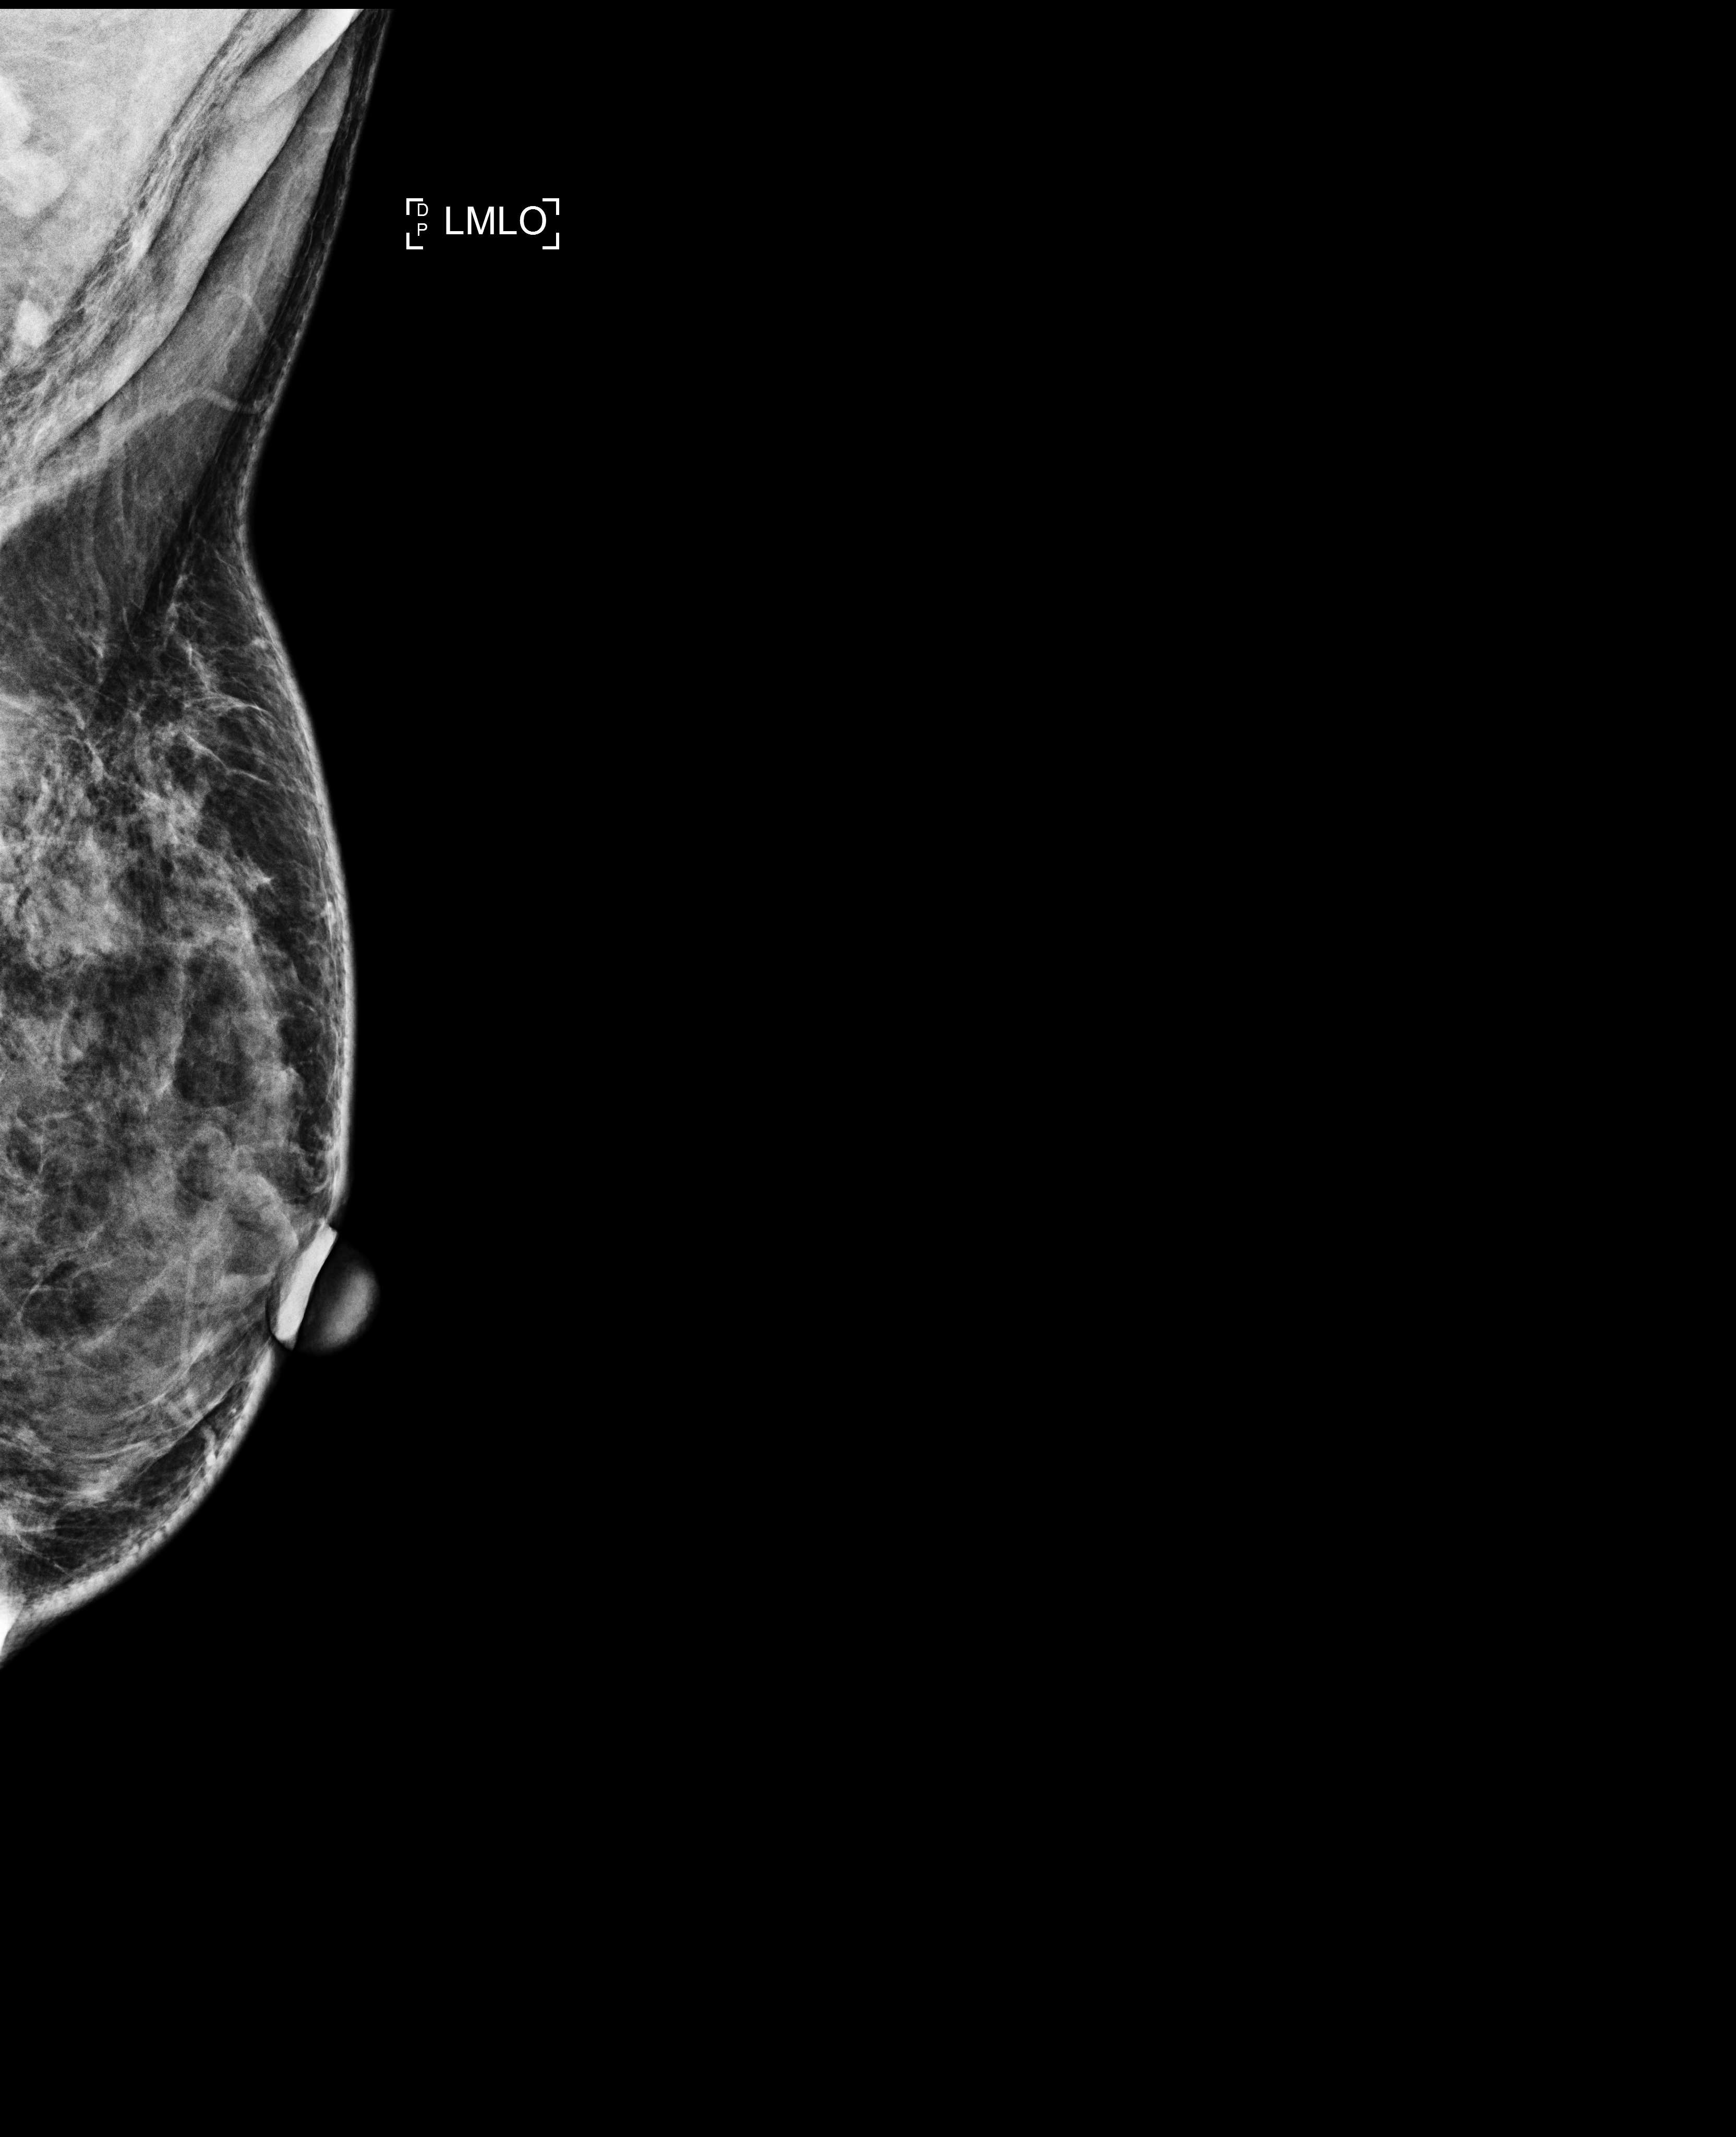
Annual screening mammography examination, system: Selenia Dimensions. Patient: female, 60 years.
Image type: full-field digital mammogram. Breast: left. Projection: MLO view.